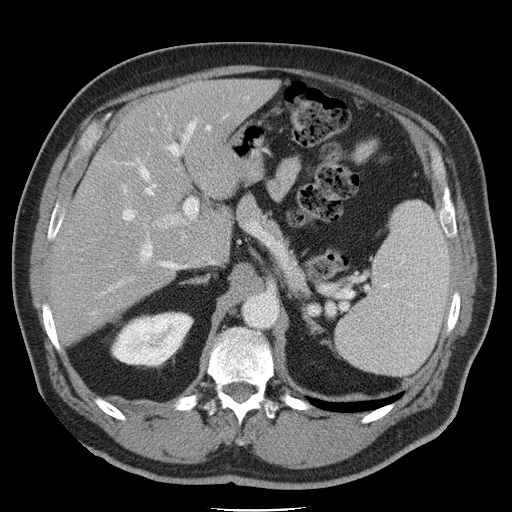
Contrast-enhanced abdominal CT, one axial slice; 120 kVp; soft-tissue window (W 400 / L 40 HU); 5 mm slice thickness; 512 × 512 image matrix, field of view 386 × 386 mm. Male patient, age 65 years. Case-level facts recorded for this patient, not image findings: diagnosis: colorectal cancer liver metastases, imaged before liver resection; multiple liver metastases: yes; largest metastasis: 4.9 cm; disease in both lobes: no.
Outlined on this slice (outlined manually by an expert reader):
- hepatic veins: bounding box <136,113,230,270> (left, top, right, bottom; pixels)
- liver: <56,80,272,340>
- planned liver remnant (the part of the liver to remain after resection): <104,80,272,252>
- portal vein (with intrahepatic branches): <117,120,199,287>